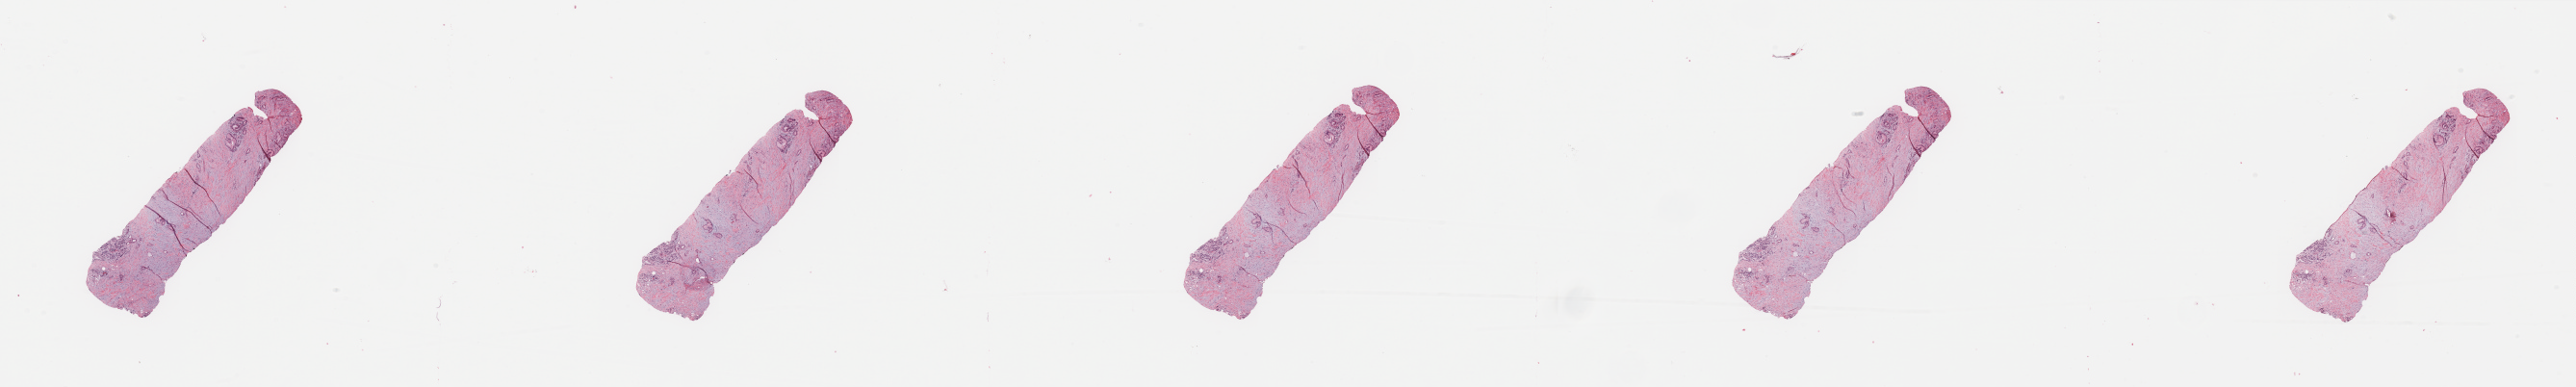
Whole-slide histology image, Hematoxylin and eosin (H&E) stained, whole scanned area (about 42.3 x 6.4 mm, acquisition: 20x scan) shown as a low-resolution overview. Tumour tissue sample, sampled site: pancreas. 74-year-old male patient. Histologic grade: G1 (well differentiated). Composition of this section per pathologist review: tumour nuclei 20%, necrosis 0%.
Histologic diagnosis: Infiltrating duct carcinoma, NOS. AJCC pathologic stage: IB.